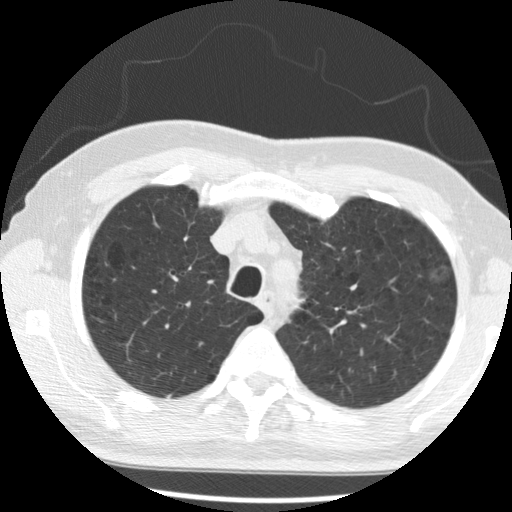
Low-dose screening chest CT, axial slice, second screening round (one year after baseline), lung window (W 1500 / L -600 HU), 2.5 mm slice thickness, slice 64 of 285 in the series. Male, age 68 years at enrolment.
Expert reader's lesion annotation, bounding box [x1, y1, x2, y2] px = [416, 260, 461, 295]. Screening reader's record for this exam (one nodule recorded; not confirmed to be the boxed lesion): non-calcified nodule or mass ≥4 mm, left upper lobe, 15 × 11 mm, poorly defined margins, ground glass attenuation, pre-existing on the prior screen: yes; interval growth: yes. Lung cancer was diagnosed 278 days after this screen: bronchiolo-alveolar adenocarcinoma, NOS, left upper lobe, moderately differentiated (G2), stage IA (AJCC 6th edition), 17 mm at pathology.